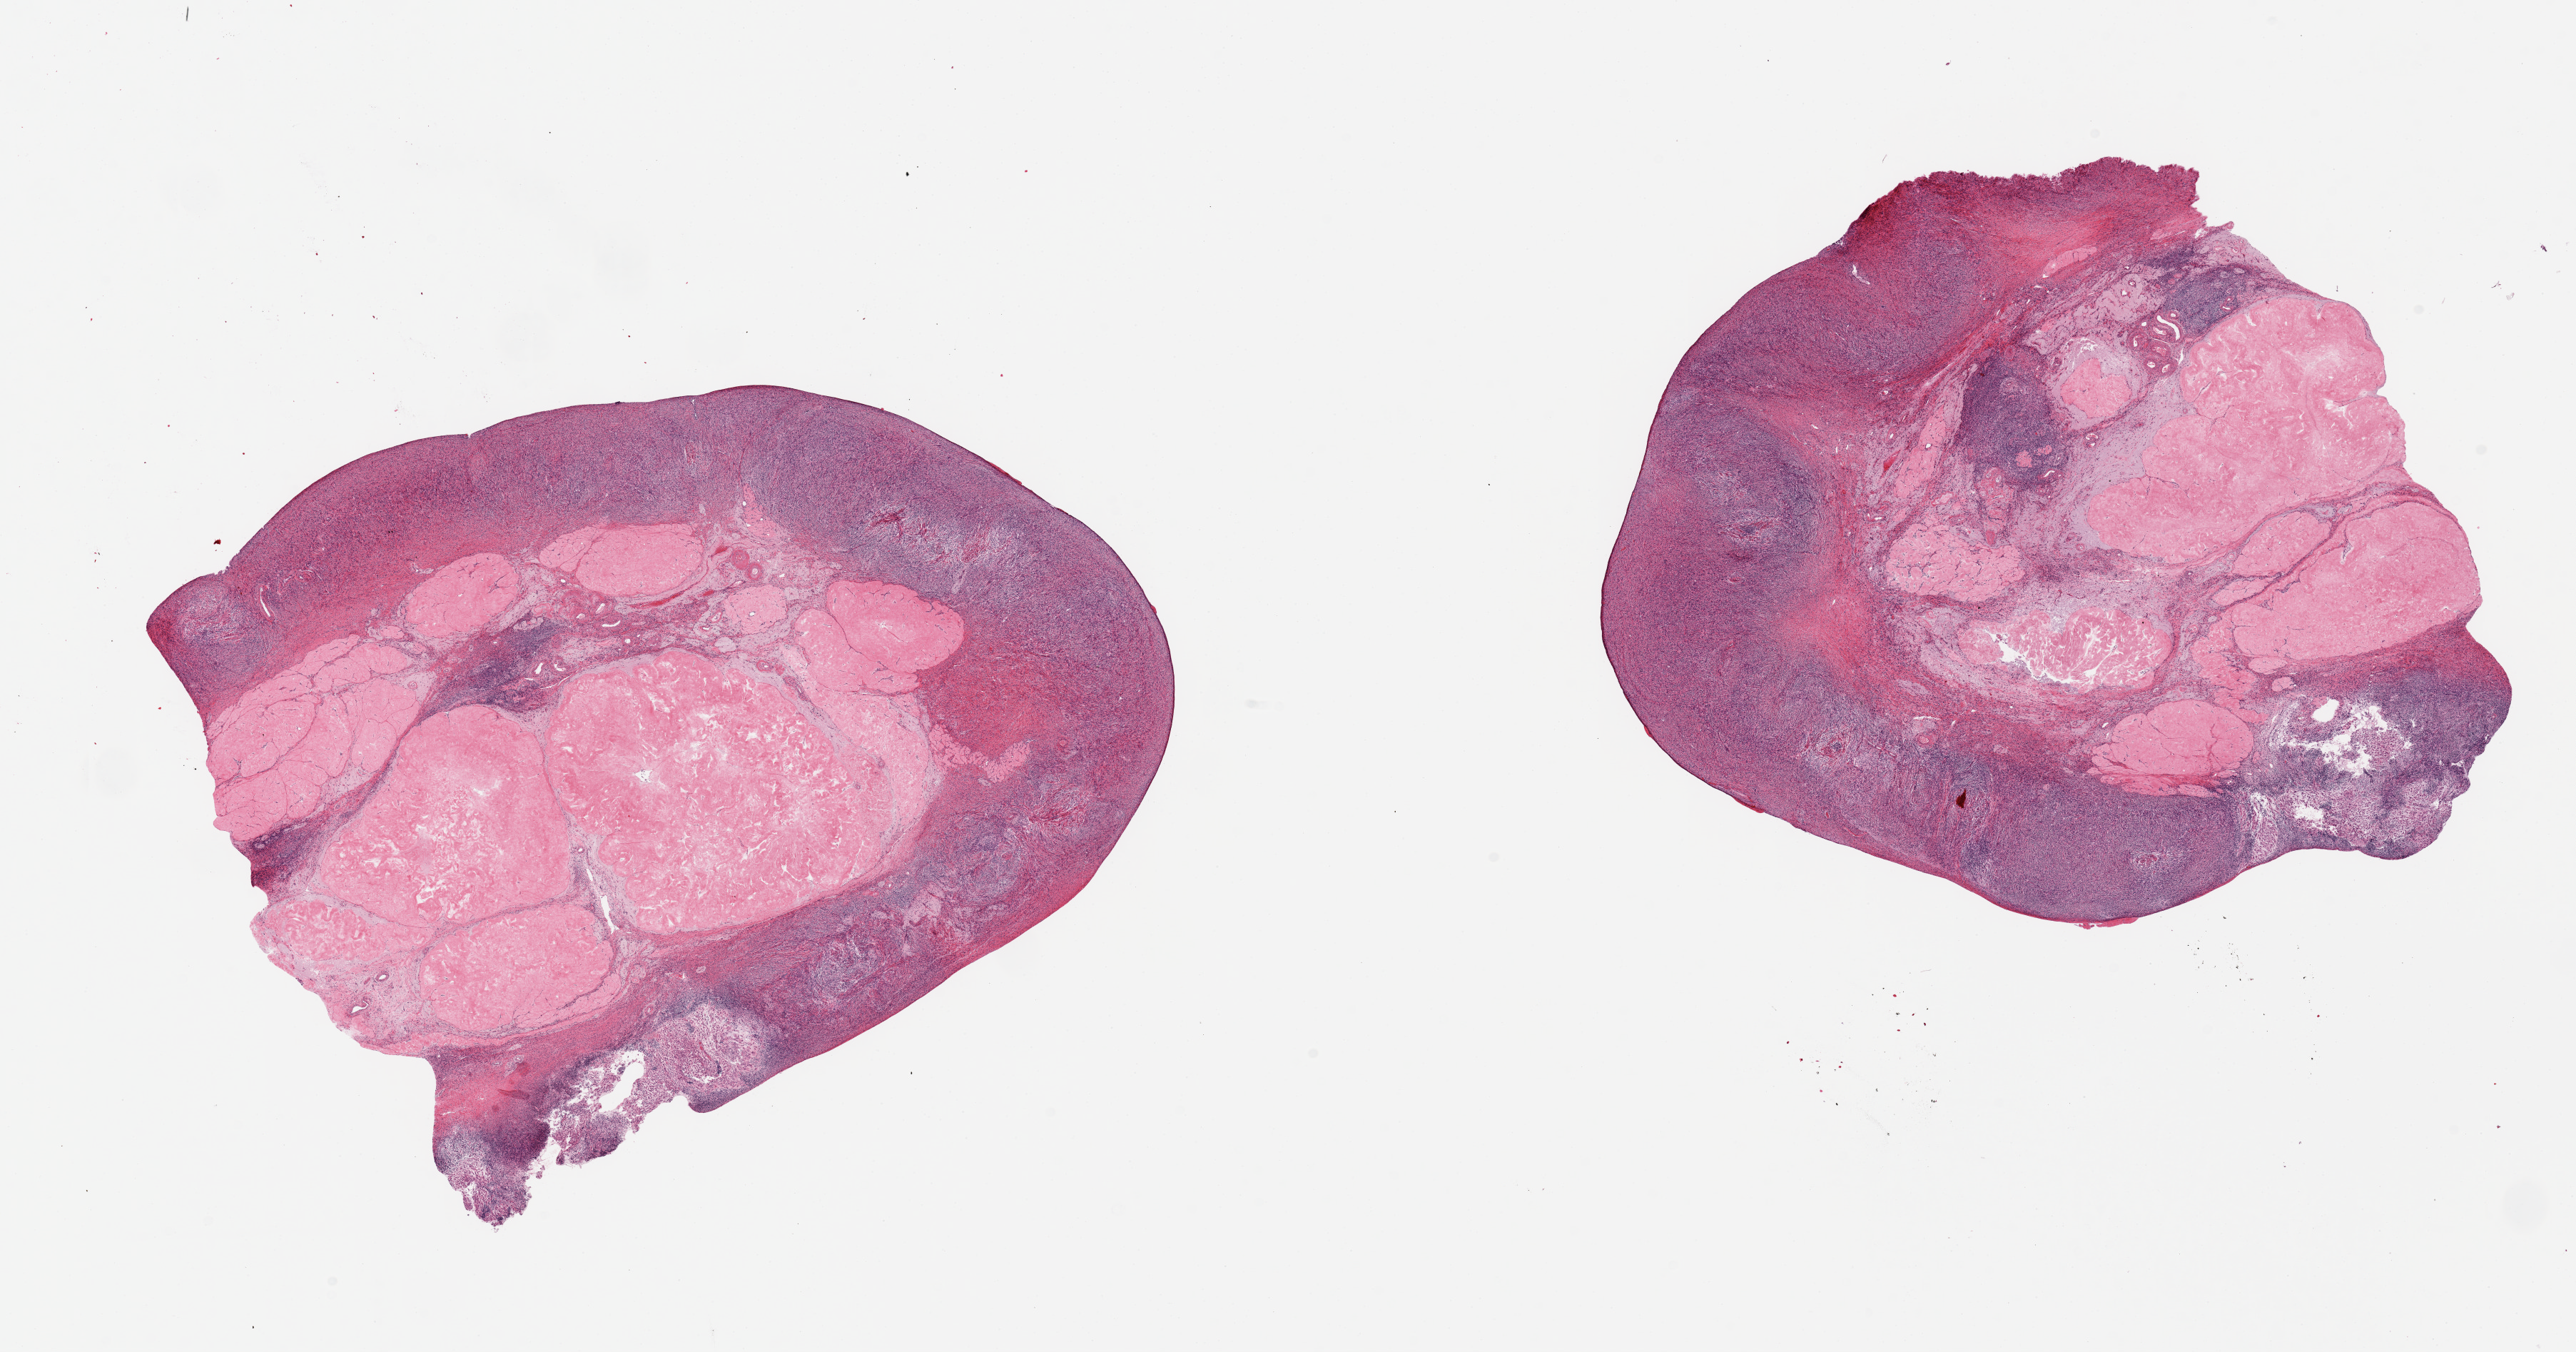
Hematoxylin and eosin (H&E) whole-slide image, brightfield, whole scanned area (about 28.5 x 15.0 mm) shown as a low-resolution overview. PAXgene-fixed paraffin-embedded (PFPE) section. Sampled site (target tissue): ovary. Tissue donor sample.
Review note (as recorded): 2 pieces, post menopausal atrophy.